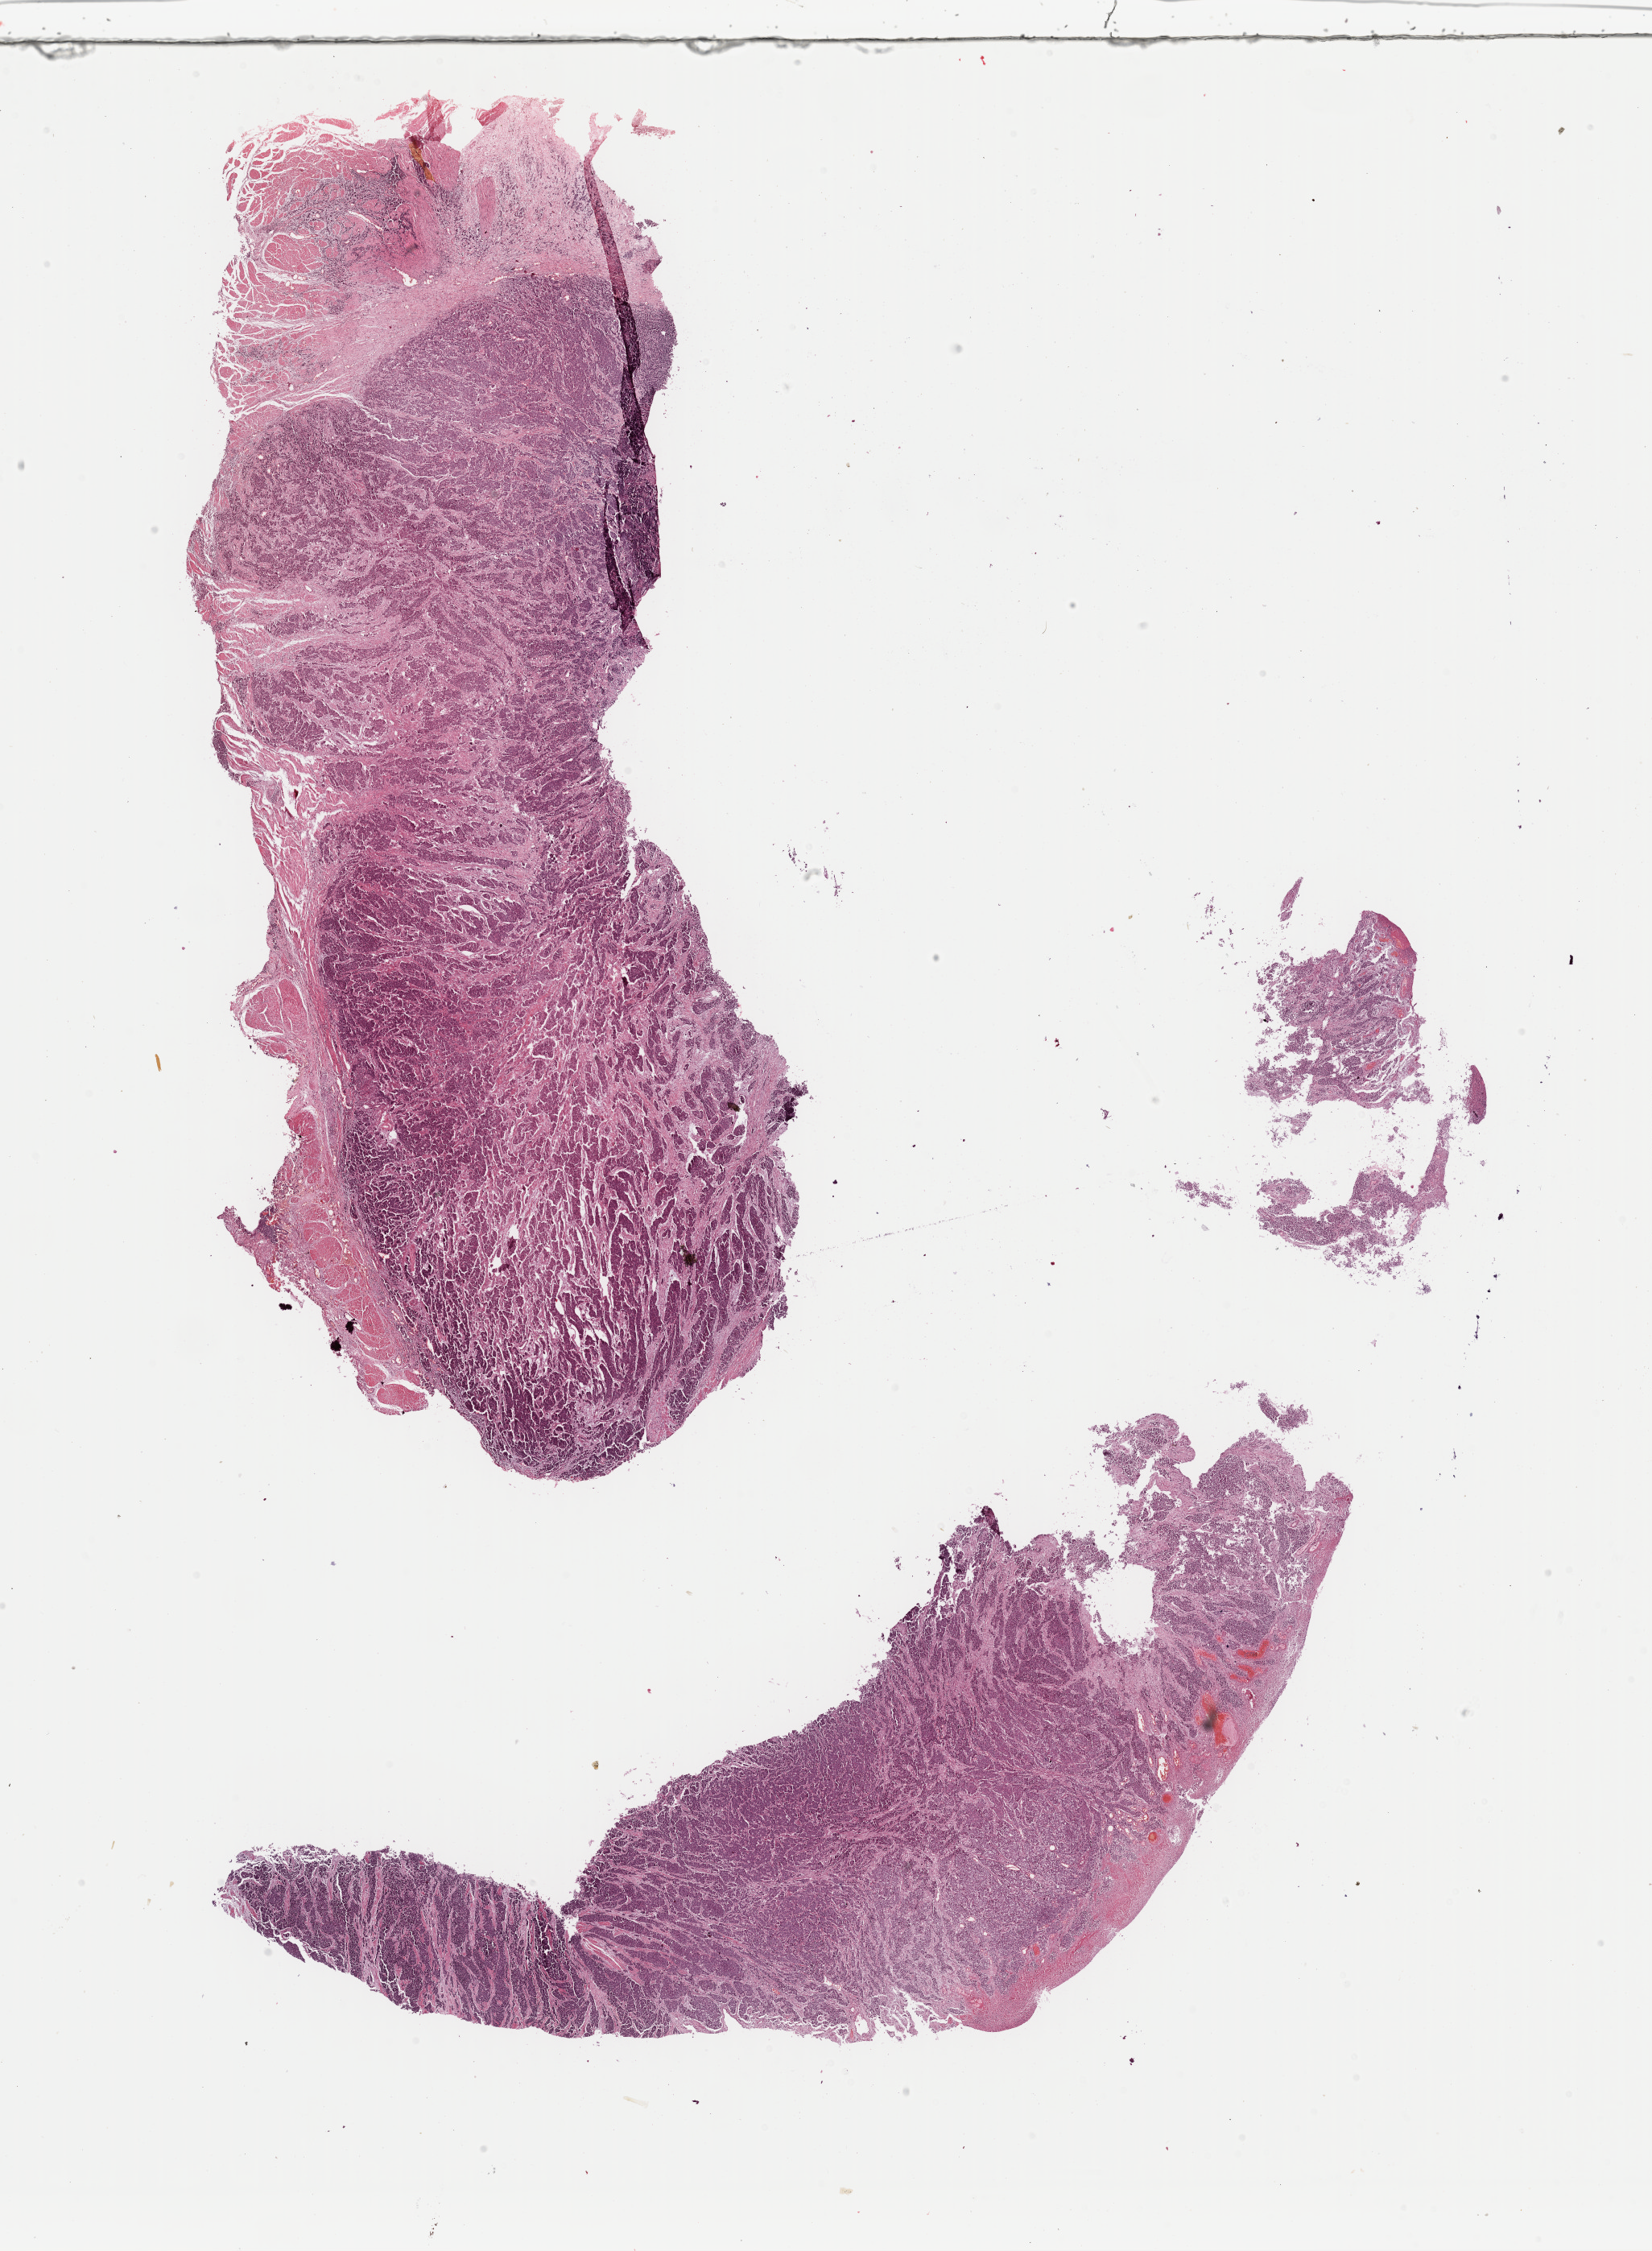
H&E whole-slide image — low-resolution overview of the scanned area, about 16.2 x 22.1 mm. FFPE section. Sample: primary tumour, esophagus. Male patient; age at initial diagnosis 49 years. Histologic grade: G3 (poorly differentiated).
• AJCC pathologic stage: IIA
• histologic diagnosis: Squamous cell carcinoma, NOS (middle third of esophagus)